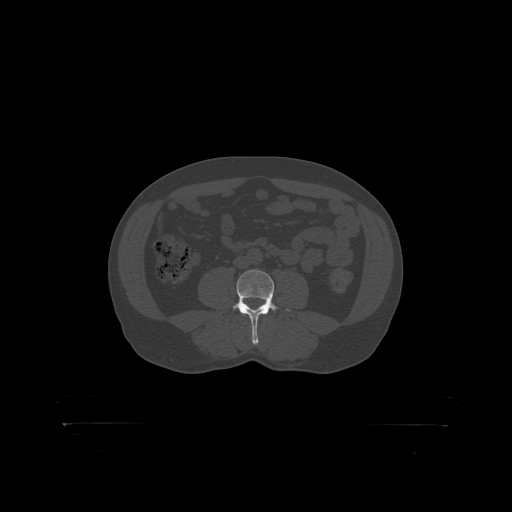
CT including the spine, one axial slice. Position 236 of 399 along the scan axis. 120 kVp. Bone window (W 1800 / L 400 HU). 1.25 mm slice thickness. 512 × 512 image matrix, field of view 650 × 650 mm. Male patient, age 46 years. From the clinical record (not read from this slice): primary cancer: skin.
Outlined on this slice (semi-automatic segmentation, software-assisted and operator-edited):
- L4 vertebra: bounding box [x1, y1, x2, y2] px = [233, 270, 288, 319]